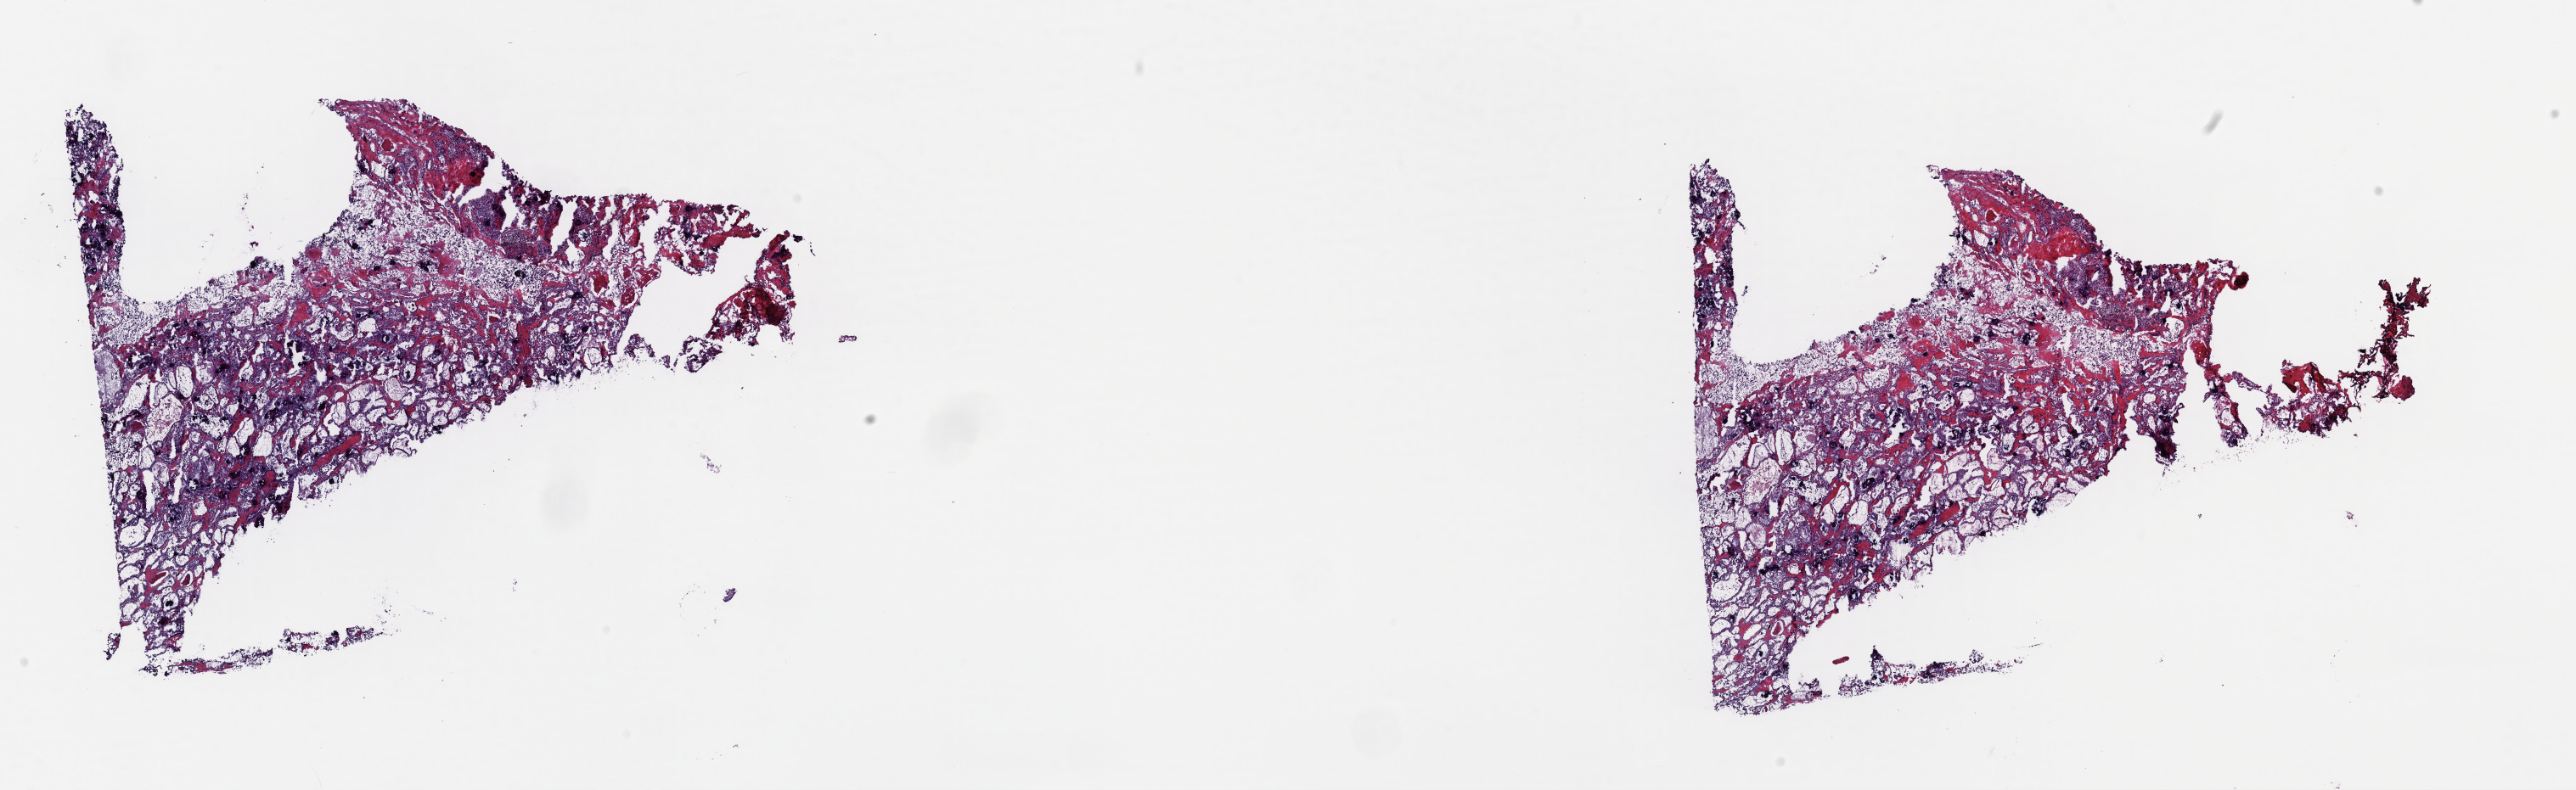
Whole-slide histology image, Hematoxylin and eosin (H&E) stained — whole scanned area (about 24.0 x 7.4 mm) shown as a low-resolution overview, frozen section from the top of the tissue portion, sample: primary tumour, thyroid. Male patient; age at initial diagnosis 38 years. Pathologist review of this section (percent, as recorded): tumour cells 50%, tumour nuclei 100%, normal cells 0%, stromal cells 50%, necrosis 0%. Inflammatory infiltration, as recorded: lymphocyte infiltration 1%, monocyte infiltration 6%, neutrophil infiltration 0%.
TNM: T2 N0 M0. Histologic diagnosis: Papillary carcinoma, follicular variant (thyroid gland). Lymph nodes positive (case pathology): 0 of 3 examined. AJCC pathologic stage: I (6th edition). Laterality: right.